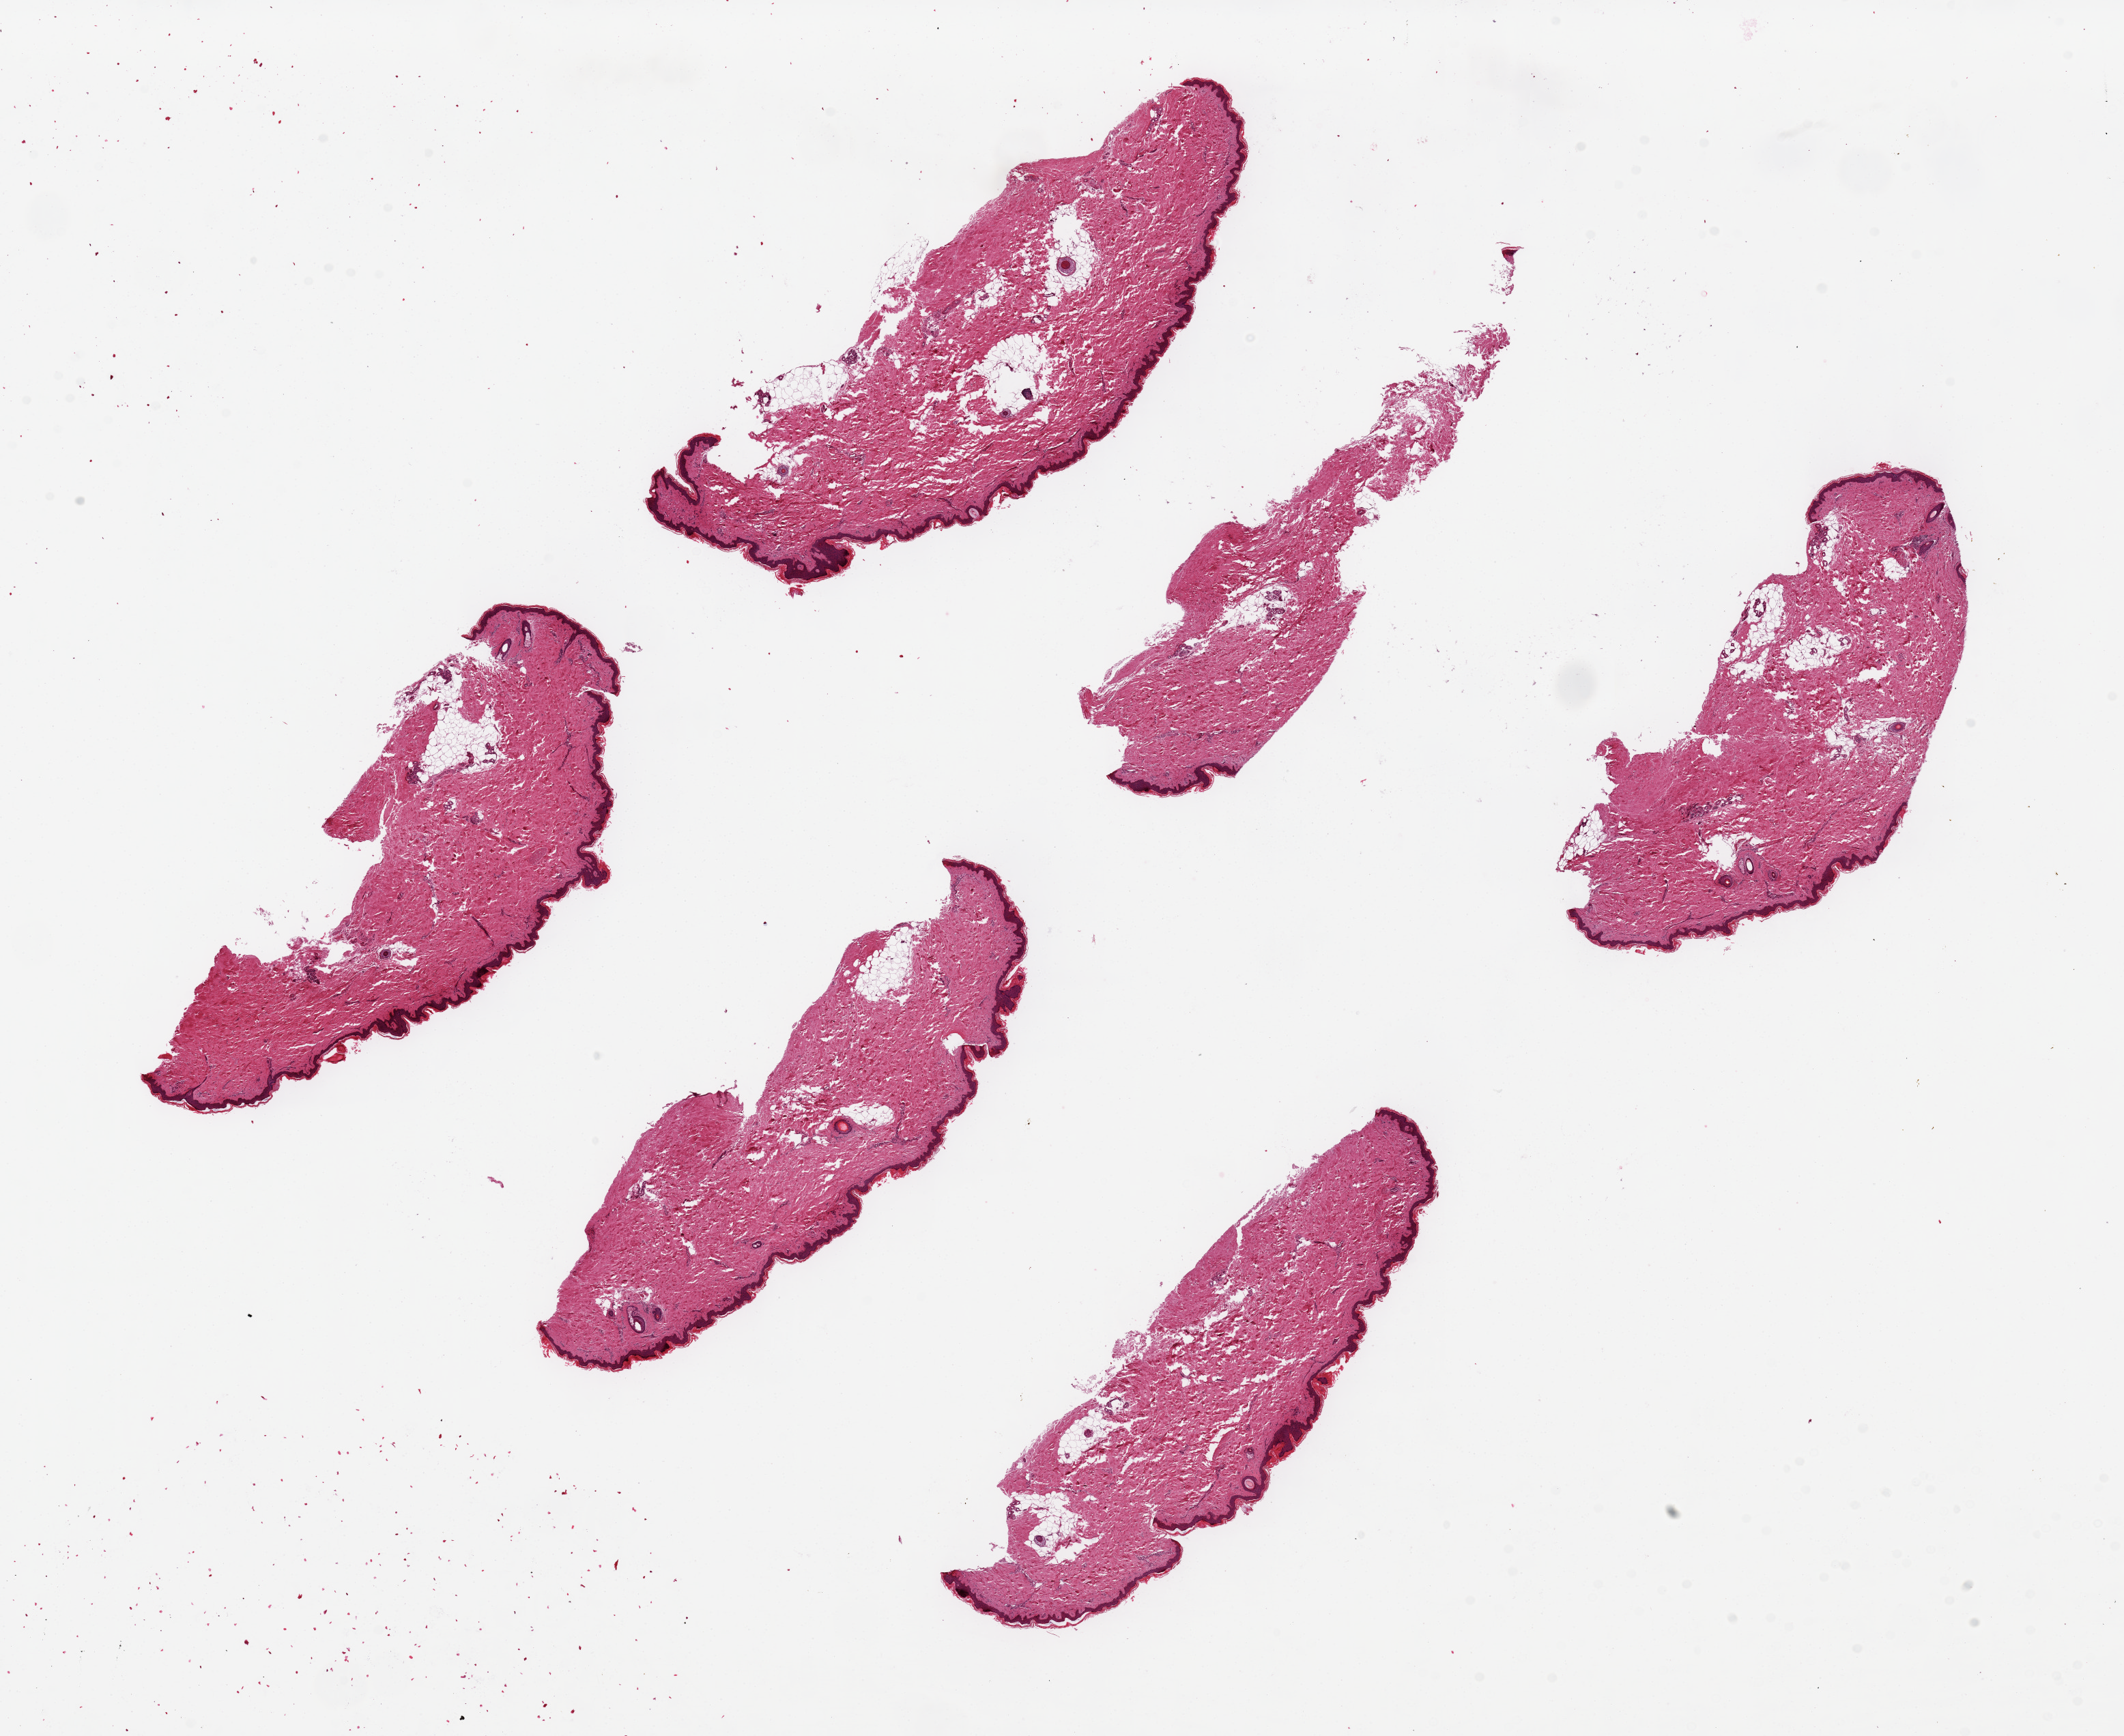
Hematoxylin and eosin (H&E) whole-slide image, whole scanned area (about 24.6 x 20.1 mm, acquisition: 20x scan) shown as a low-resolution overview. PAXgene-fixed, paraffin-embedded tissue. Section of skin of lower leg (target tissue). Donor tissue sample. Donor: female.
Pathologist's review note for this sample: 6 pieces, up to 7.5x2.5 mm; scattered dermal fractures.